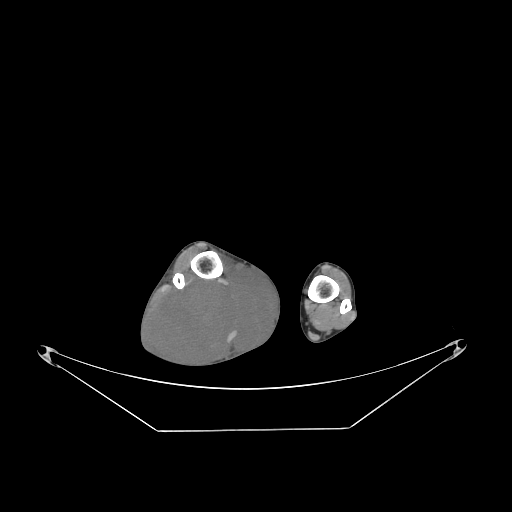
CT of an extremity soft-tissue mass (from a PET/CT study), one axial slice. Slice 60 of 267 in the series (ordered by position). 140 kVp. Soft-tissue window (W 400 / L 40 HU). 3.75 mm slice thickness. 512 × 512 image matrix. Male patient. From the clinical record (not read from this slice): histological type: liposarcoma - round cell; grade: high; site of the primary tumour: right calf.
Structures marked on this image (expert contour drawn on MRI and transferred to this co-registered scan by the dataset authors):
- gross tumour volume (mass): bounding box [x1, y1, x2, y2] px = [151, 267, 277, 368]